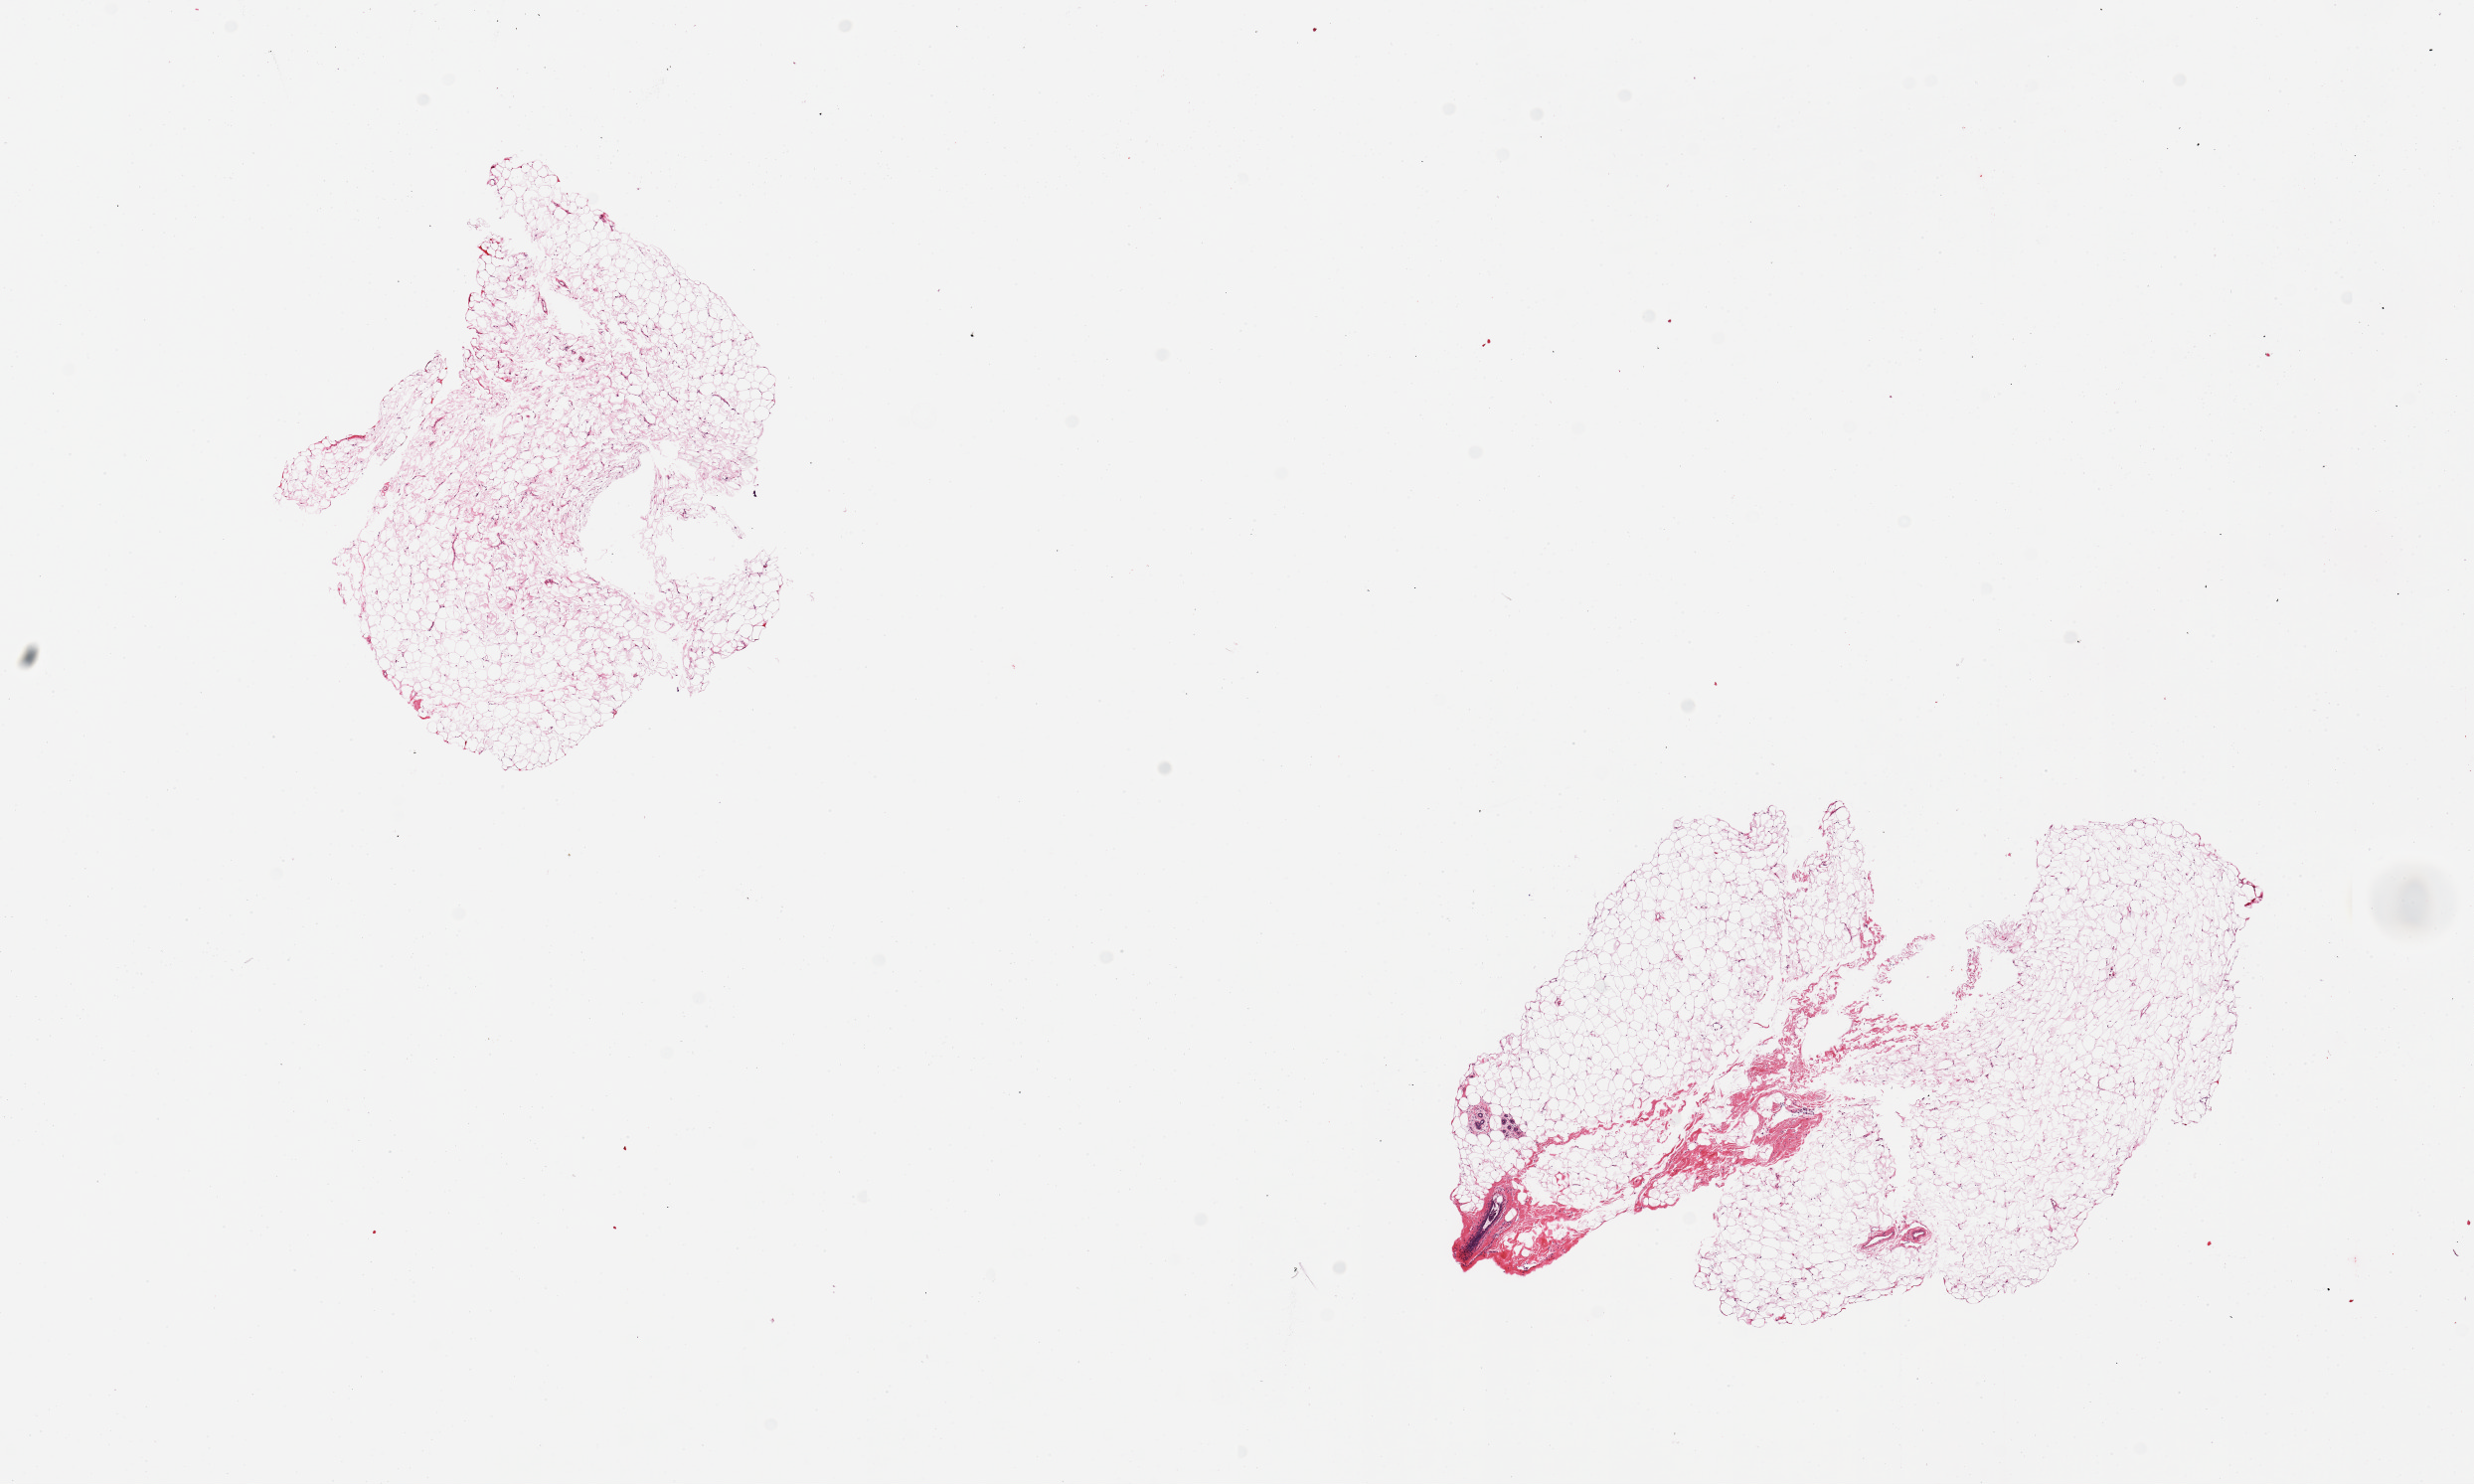
H&E whole-slide image, shown as a low-resolution overview of the whole scanned area (about 19.7 x 11.8 mm, slide scanned at 20x). PAXgene-fixed paraffin-embedded (PFPE) section. Target tissue: breast. Donor tissue sample. Donor: female.
* review note (as recorded): 2 pieces, 1 piece is predominantly fat with 5-10% fibrous component with ductal/lobular elements, 1 piece is entirely fat